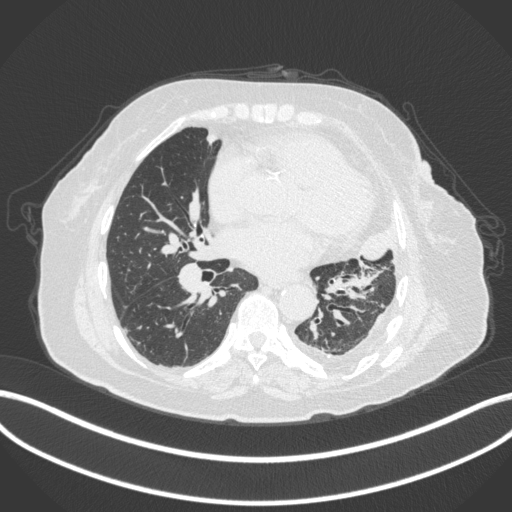
Chest CT, one axial slice; position 168 of 399 along the scan axis; lung window (W 1500 / L -600 HU); 1 mm slice thickness; 512 × 512 image matrix, field of view 400 × 400 mm. Female patient, age 75 years. Case-level facts recorded for this patient, not image findings: clinical TNM (as recorded): T3 N3 M1.
Structures marked on this image (rectangle marked by the reading radiologist):
- lung tumour (recorded histology: adenocarcinoma): bounding box [x1, y1, x2, y2] px = [355, 221, 393, 259]